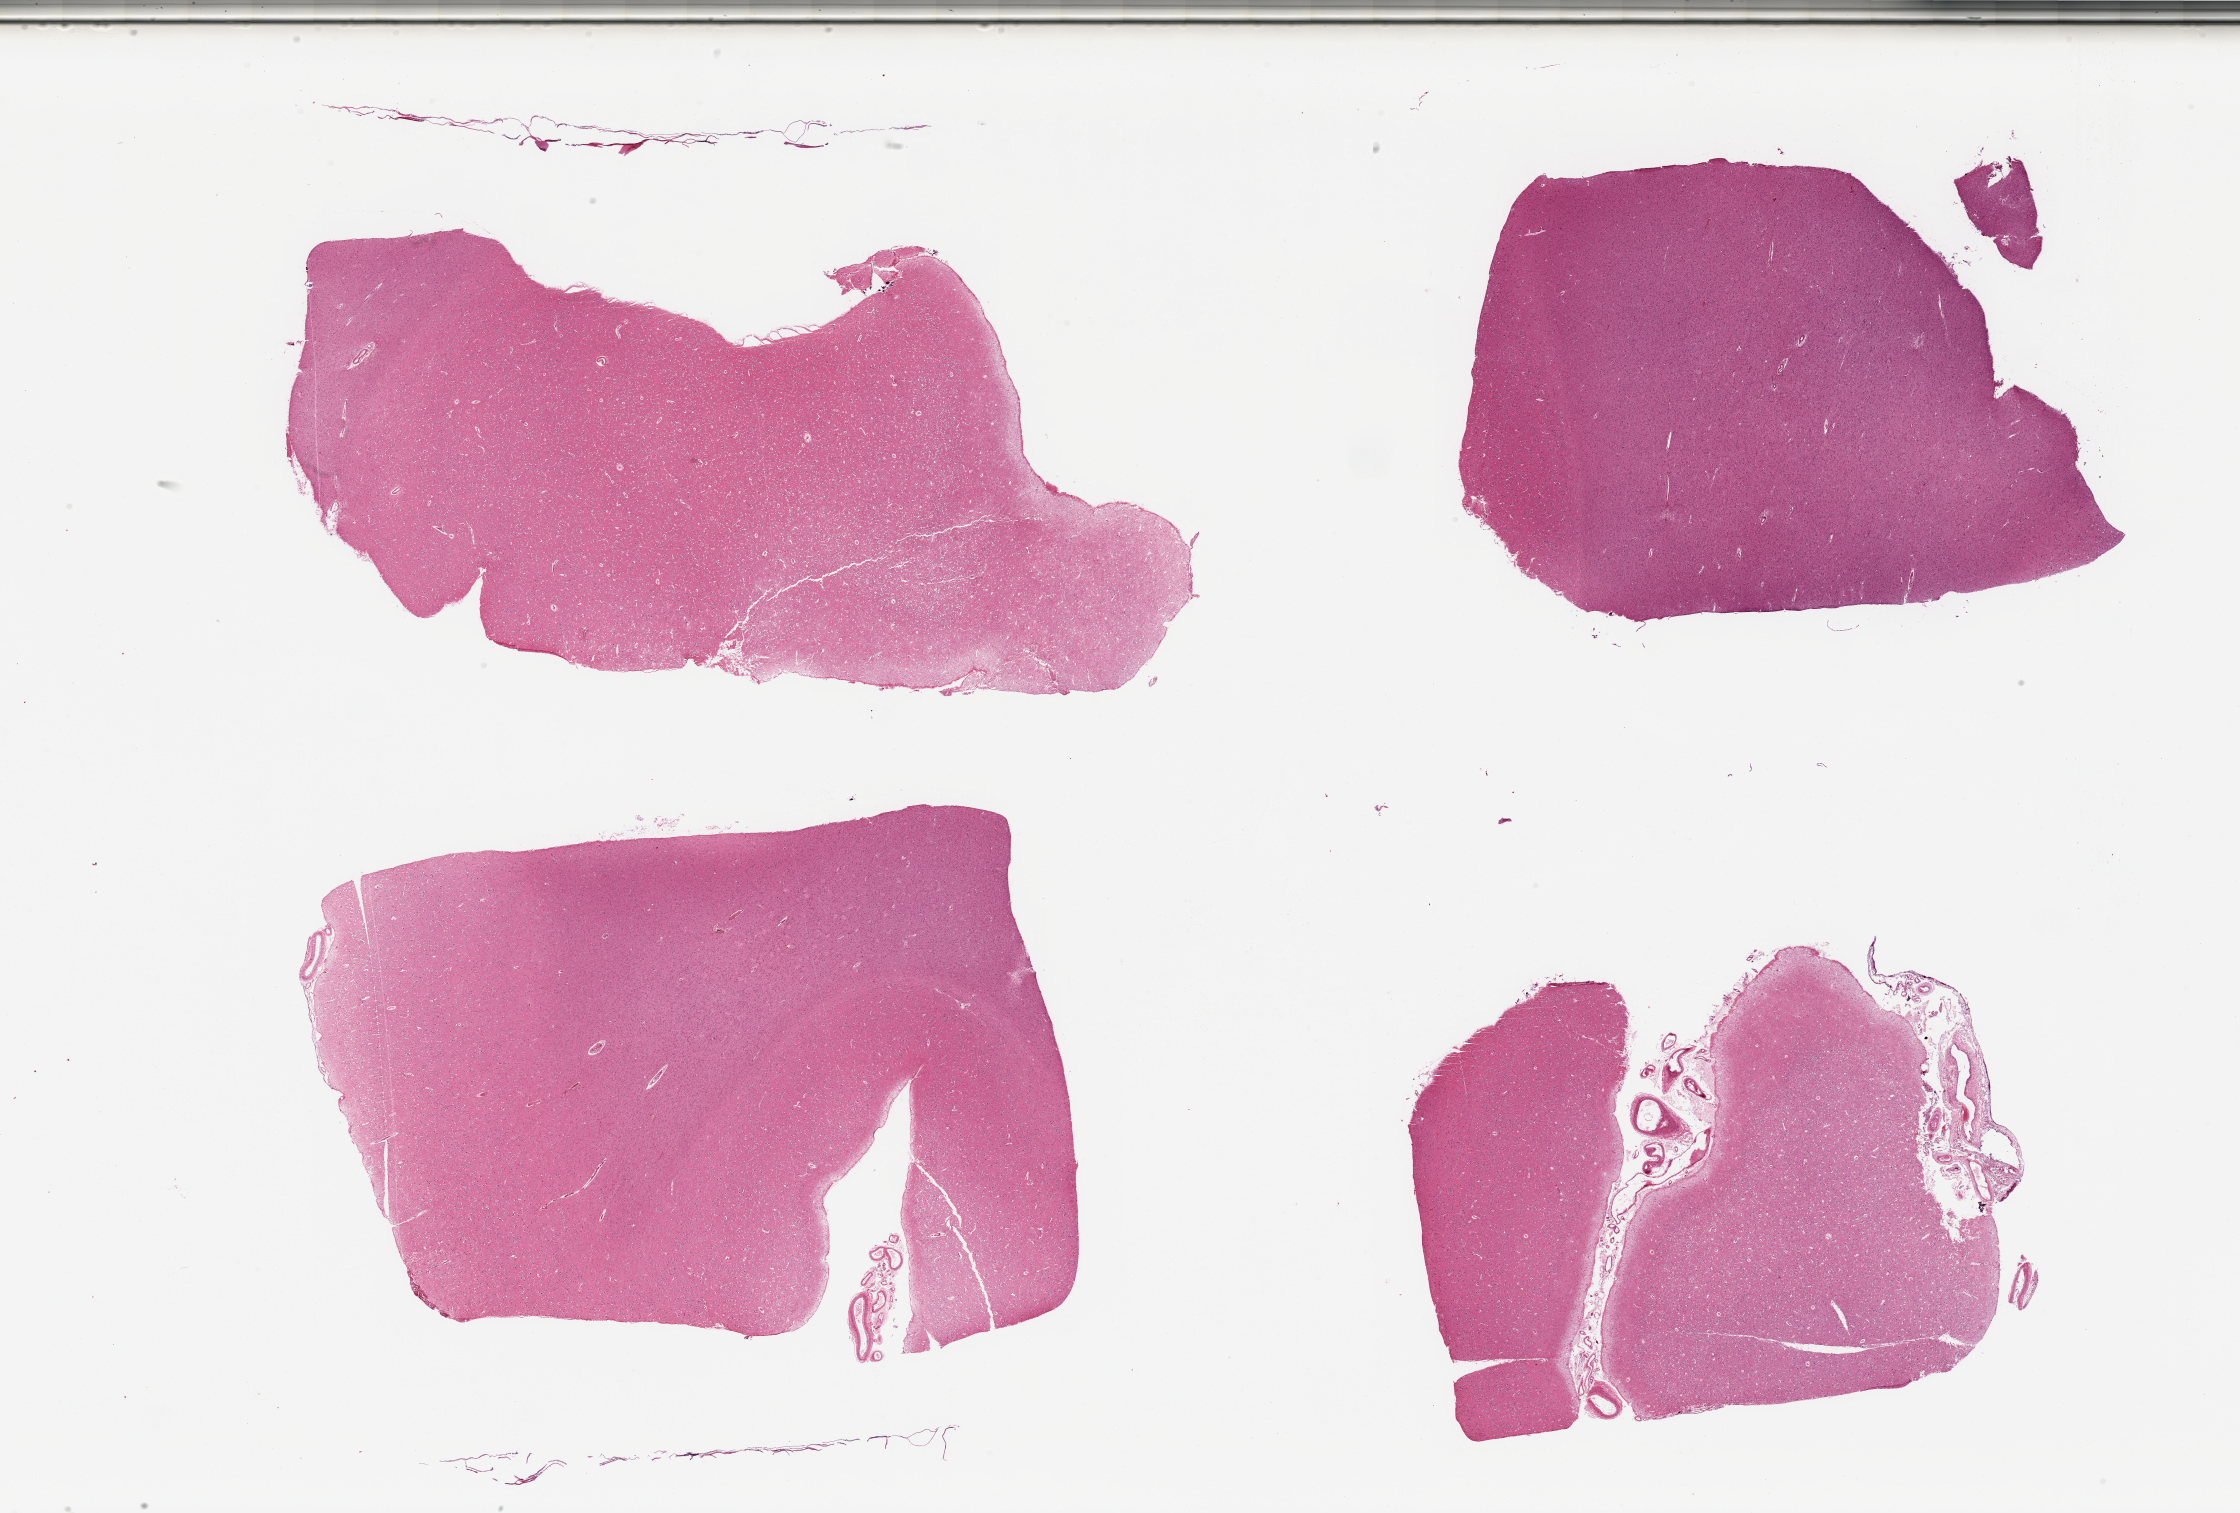
Whole-slide image, H&E stain — whole scanned area (about 35.4 x 23.9 mm, from a 20x scan) shown as a low-resolution overview, PAXgene-fixed, paraffin-embedded tissue, section of cerebral cortex (target tissue), tissue donor sample. Donor: male.
* pathologist's review note for this sample: 4 pieces; two pieces with remnants of meninges